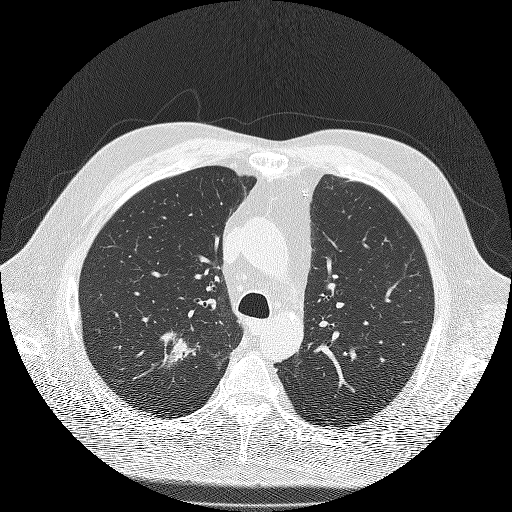
Low-dose screening chest CT, one axial slice. Slice 140 of 180 in the series (ordered by position). Reconstruction kernel FC51. Lung window (W 1500 / L -600 HU). 2 mm slice thickness. 512 × 512 image matrix, field of view 385 × 385 mm.
Structures marked on this image (outlined manually by an expert reader):
- lesion 1 (tumor, upper lobe of right lung): bounding box (x1, y1, x2, y2) in pixels: (161, 332, 196, 367)